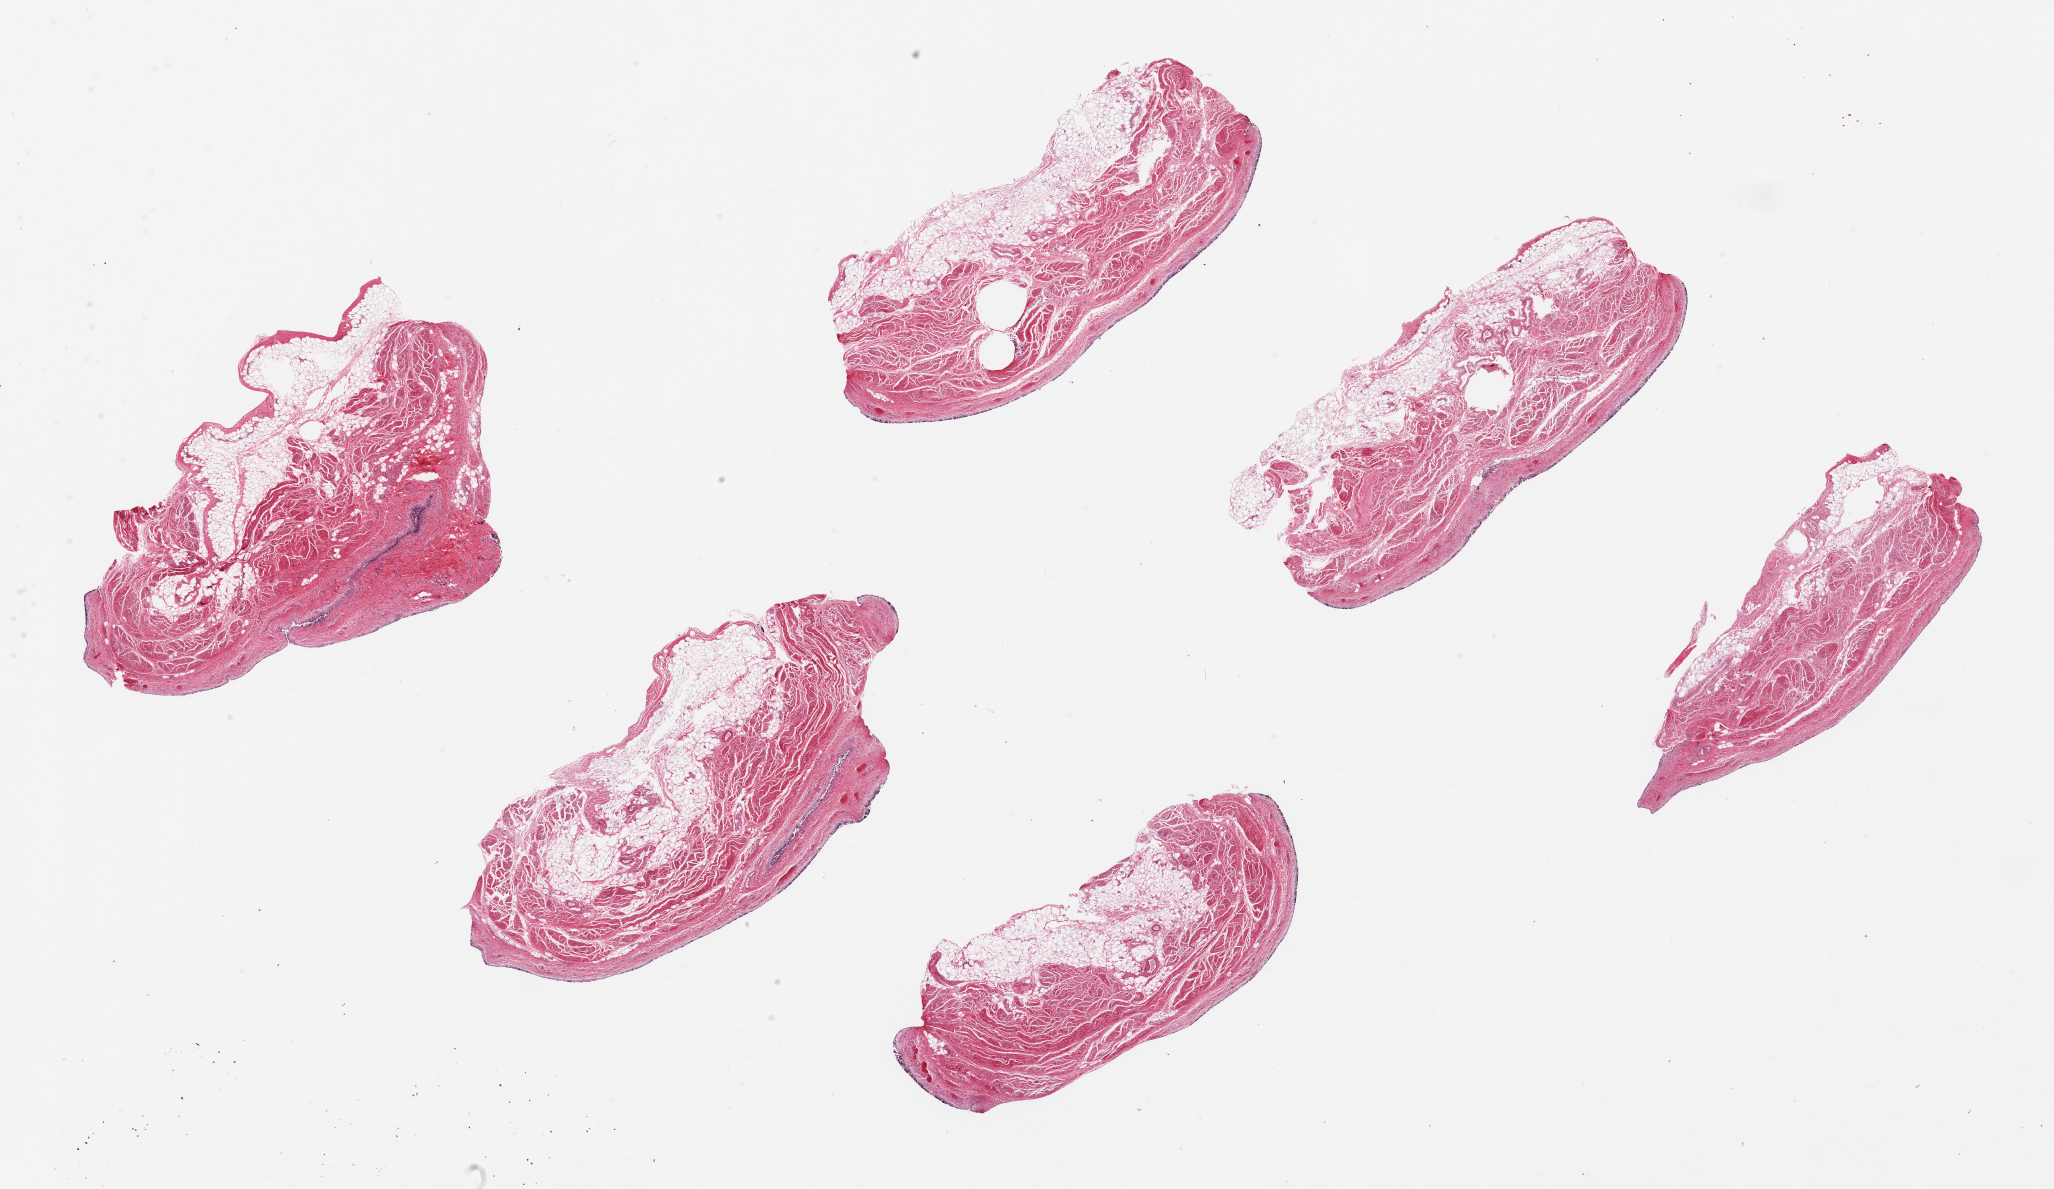
Hematoxylin and eosin (H&E) whole-slide image, whole scanned area (about 32.5 x 18.8 mm, from a 20x scan) shown as a low-resolution overview. PAXgene-fixed paraffin-embedded (PFPE) section. Target tissue: urinary bladder. Tissue donor sample. Female donor.
Pathologist's review note for this sample: 6 pieces up to 8x4 mm; epithelium largely sloughed.